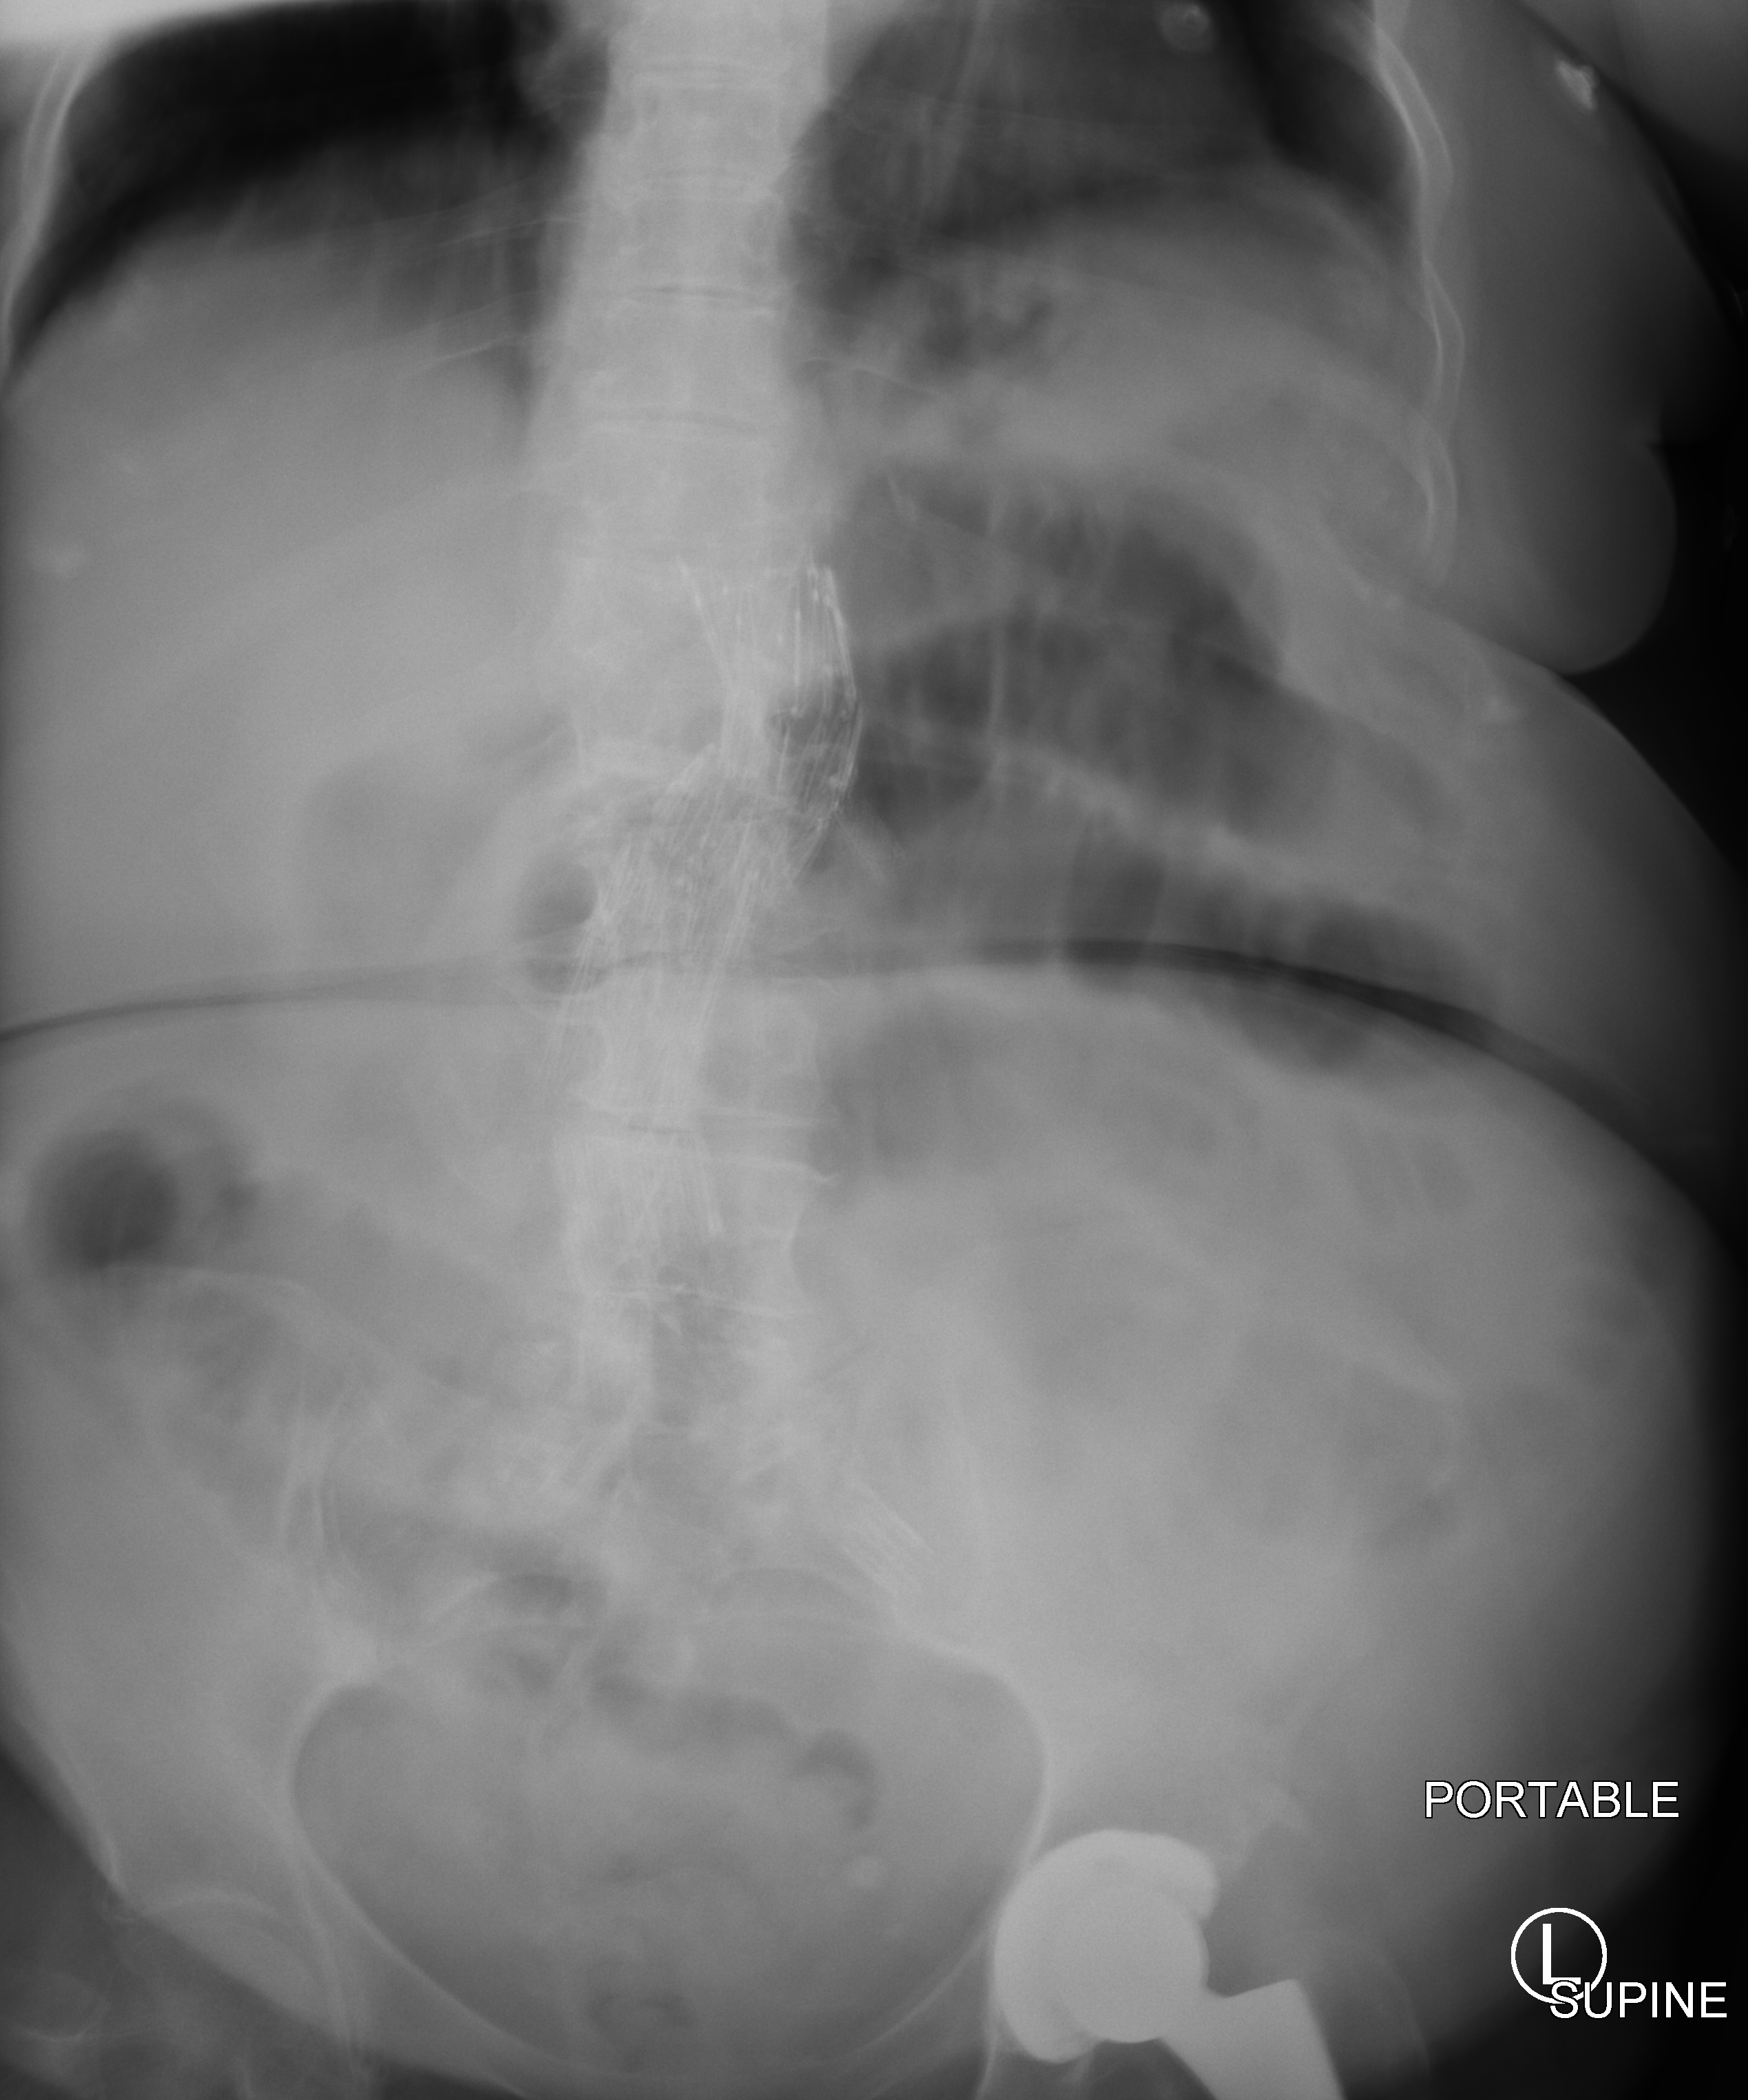
Abdomen X-ray (portable); anteroposterior (AP) projection. Female patient hospitalised with COVID-19, age 60–74 years.
From the hospital-stay record, not from the radiograph (when in the stay this image was taken is not recorded):
- mechanically ventilated during this hospital stay: no
- length of hospital stay: 9 days
- admitted to intensive care during this hospital stay: yes